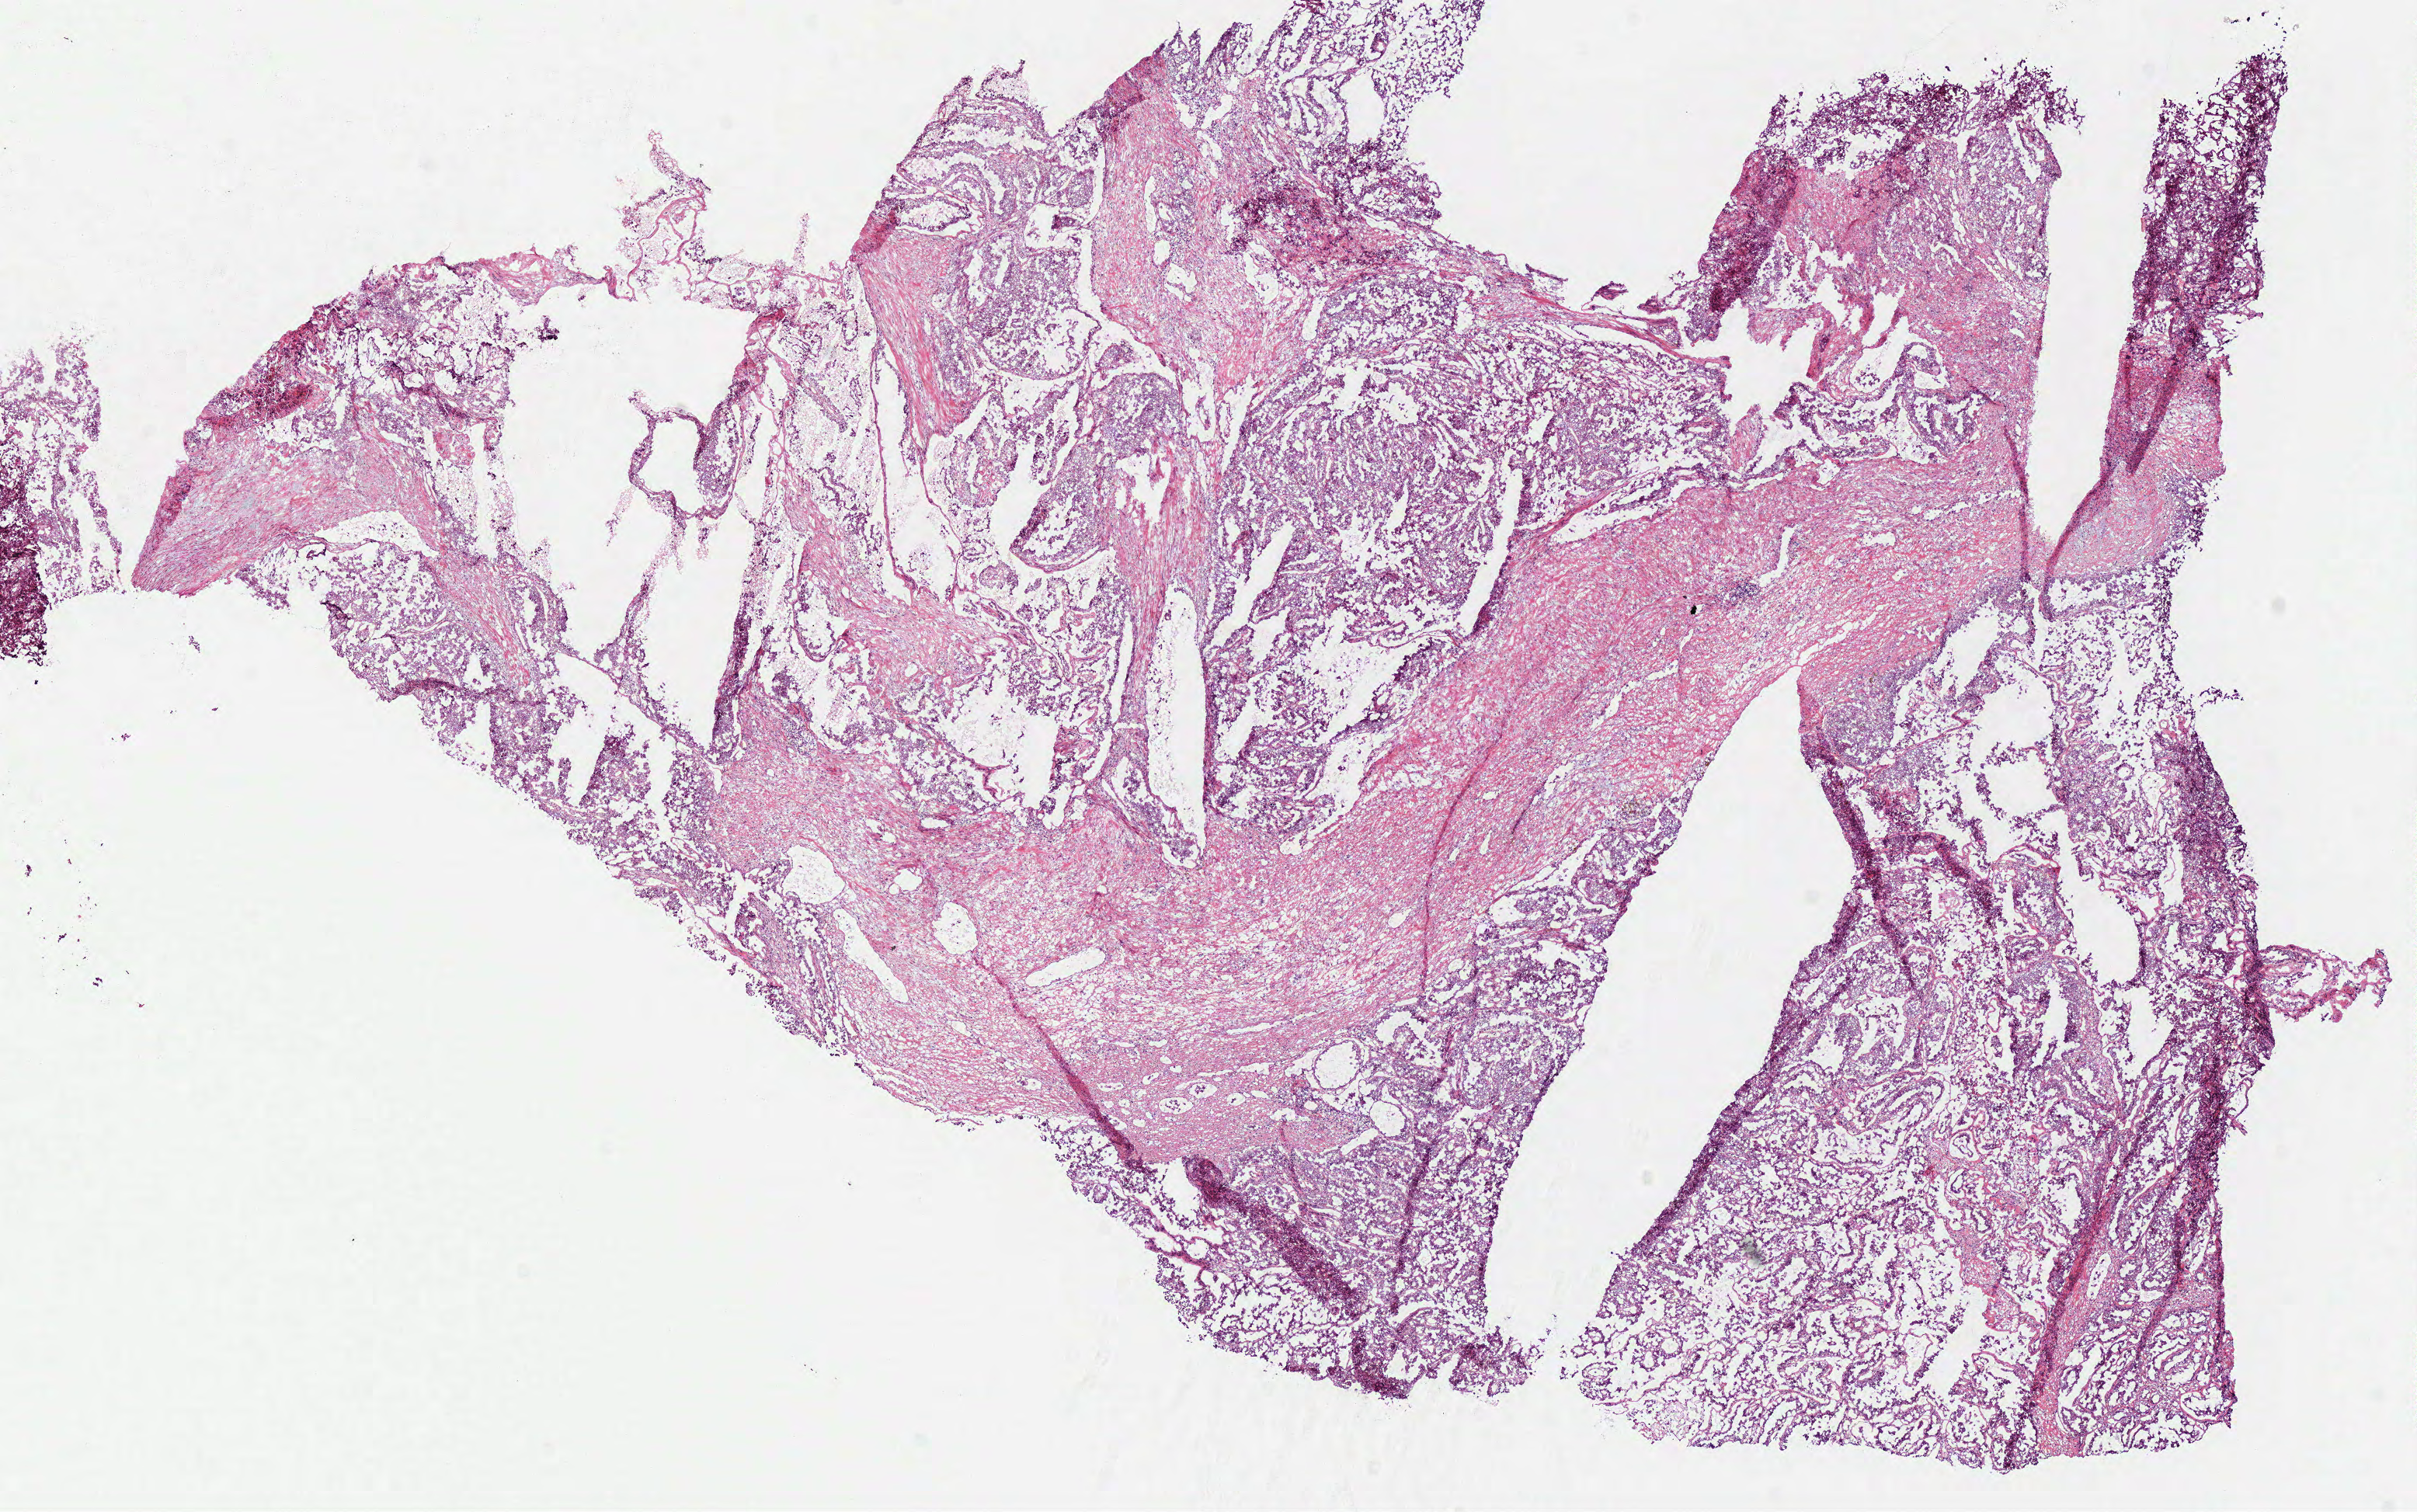
Digitized H&E tissue section (whole slide) — shown as a low-resolution overview of the whole scanned area (about 12.2 x 7.7 mm, from a 40x scan), frozen section from the bottom of the tissue portion, kidney, primary tumour sample. Patient: female, age at initial diagnosis 60 years. Pathologist review of this section (percent, as recorded): tumour cells 75%, tumour nuclei 80%, normal cells 0%, stromal cells 25%, necrosis 0%.
Laterality: left. AJCC pathologic stage: IV (6th edition). Lymph nodes positive (case pathology): 9 of 15 examined. Pathologic diagnosis: Papillary adenocarcinoma, NOS.